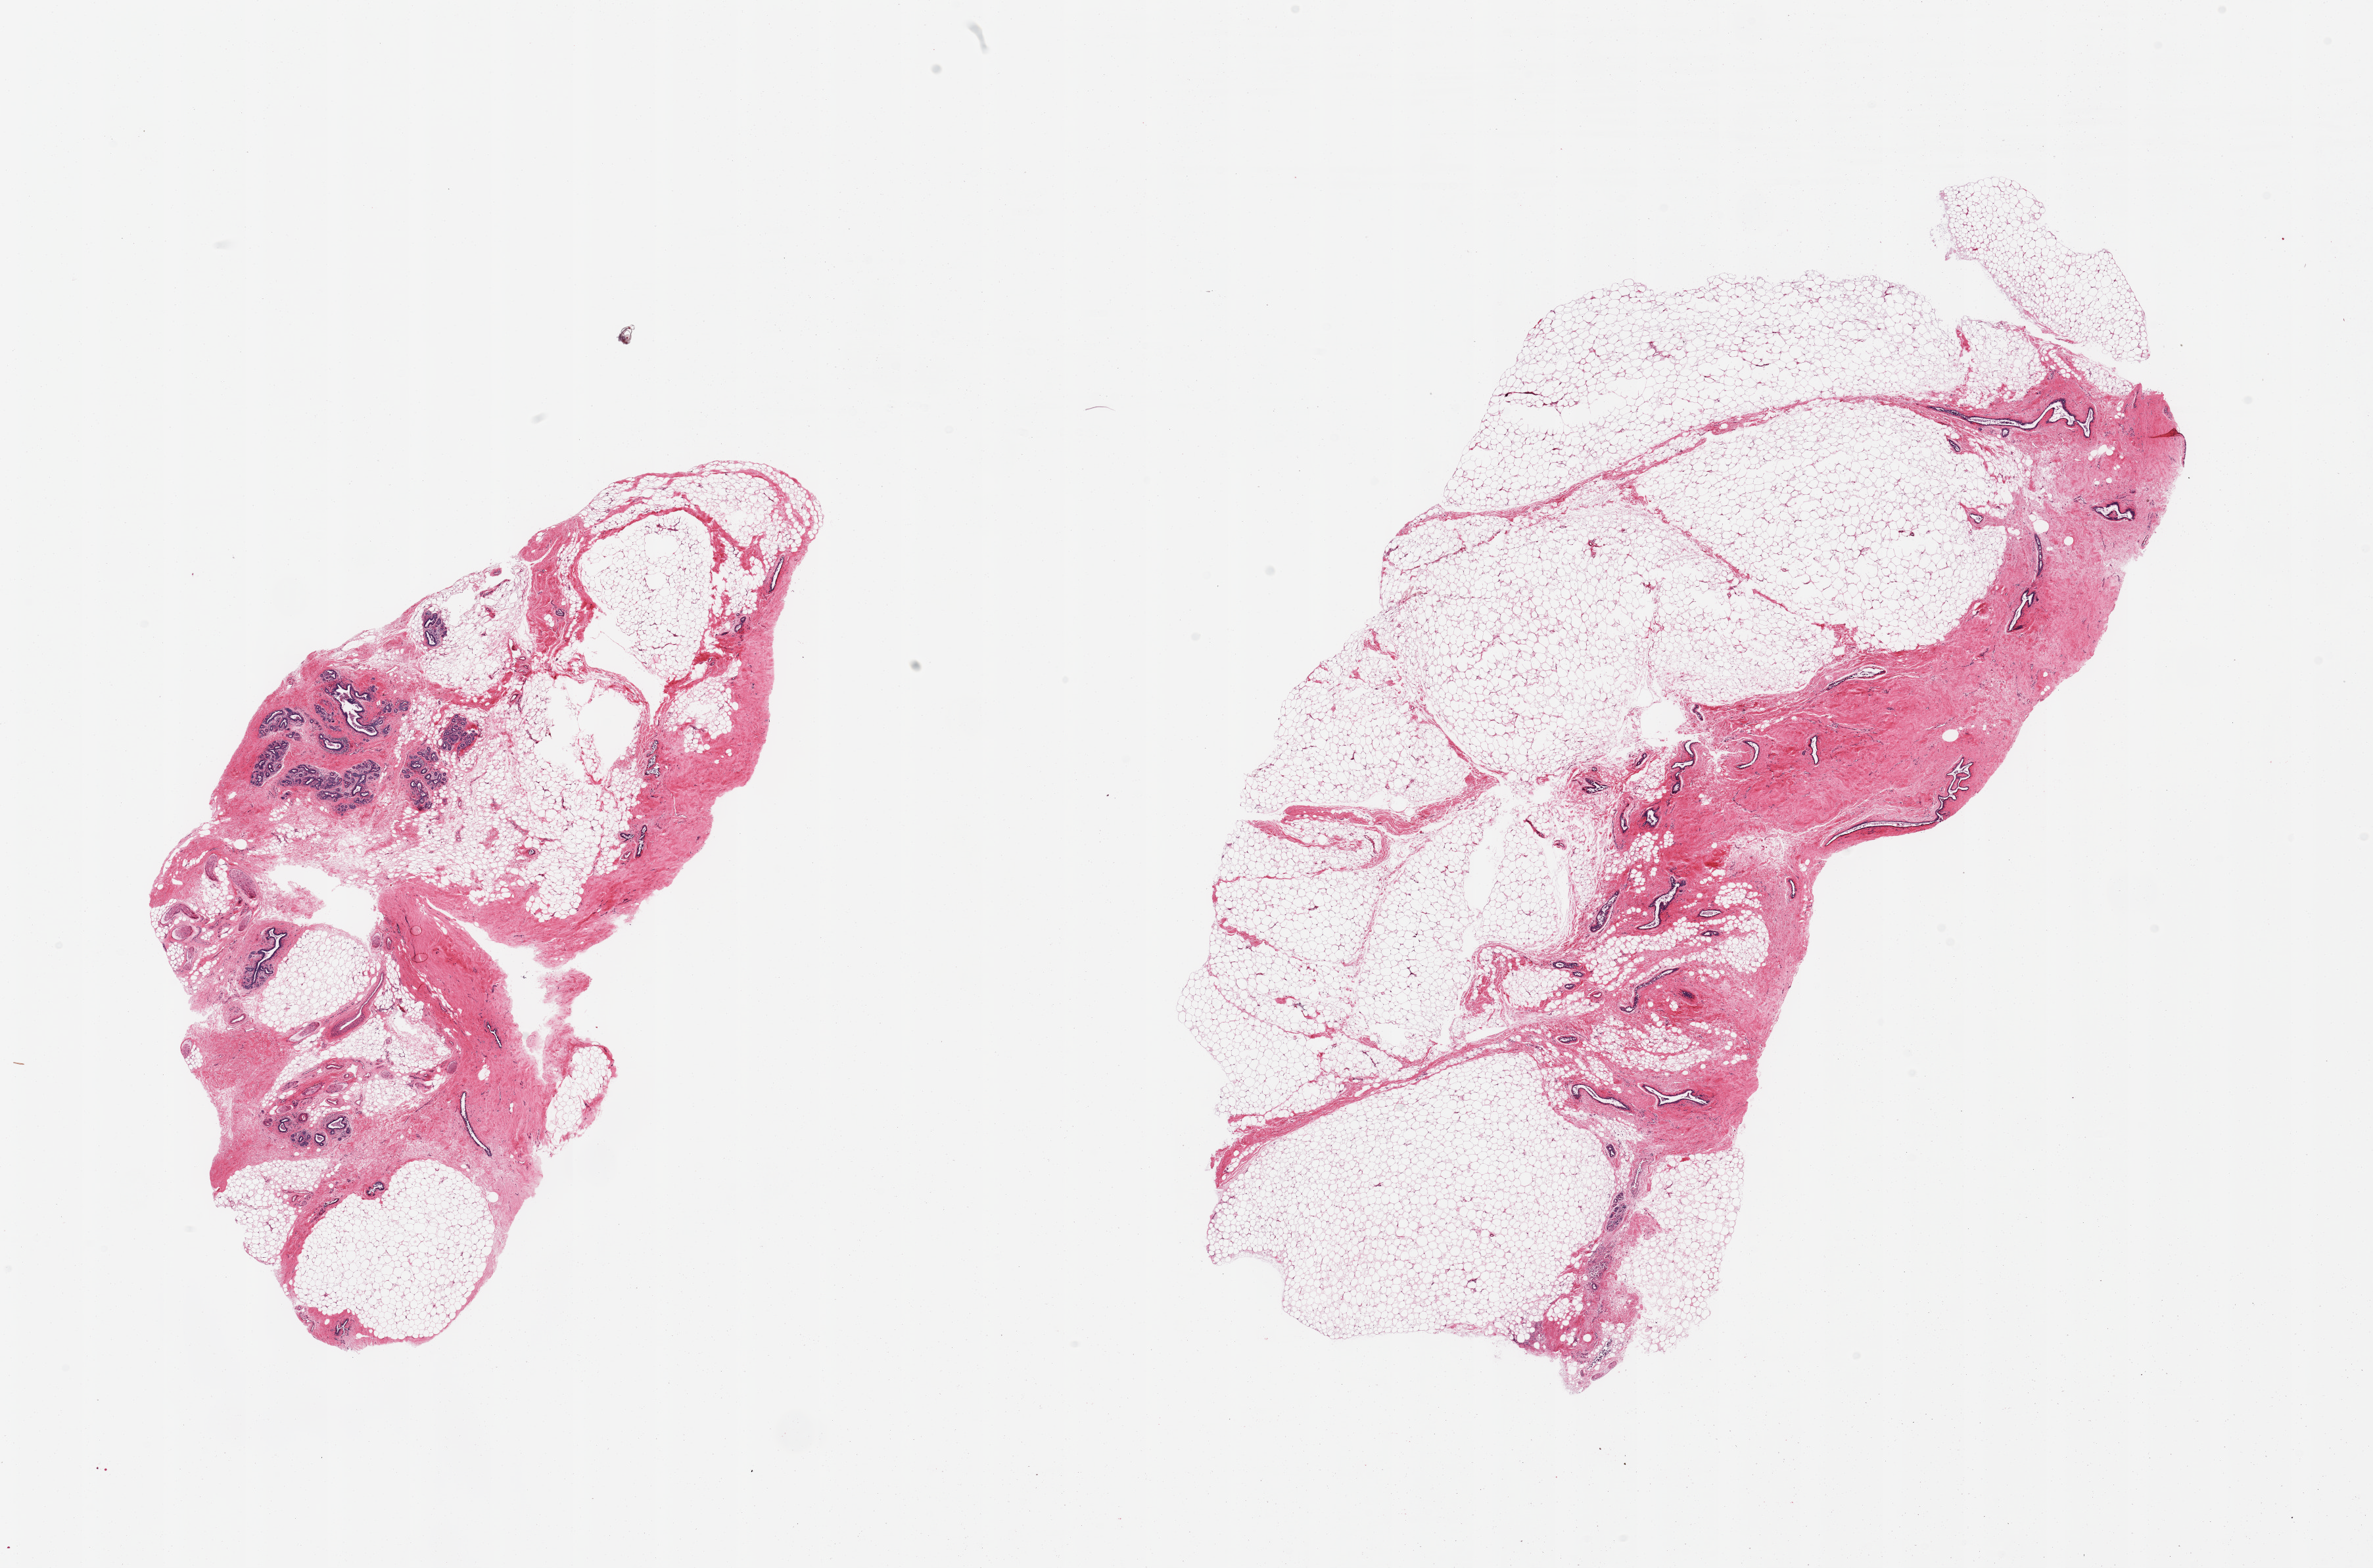
Digitized haematoxylin and eosin-stained section — low-resolution overview of the scanned area, about 28.5 x 18.9 mm (from a 20x scan); PAXgene-fixed, paraffin-embedded tissue; sampled site (target tissue): breast; tissue donor sample.
Pathologist's review note for this sample: 2 pieces; slight ductal hyperplasia in fibrofatty stroma.